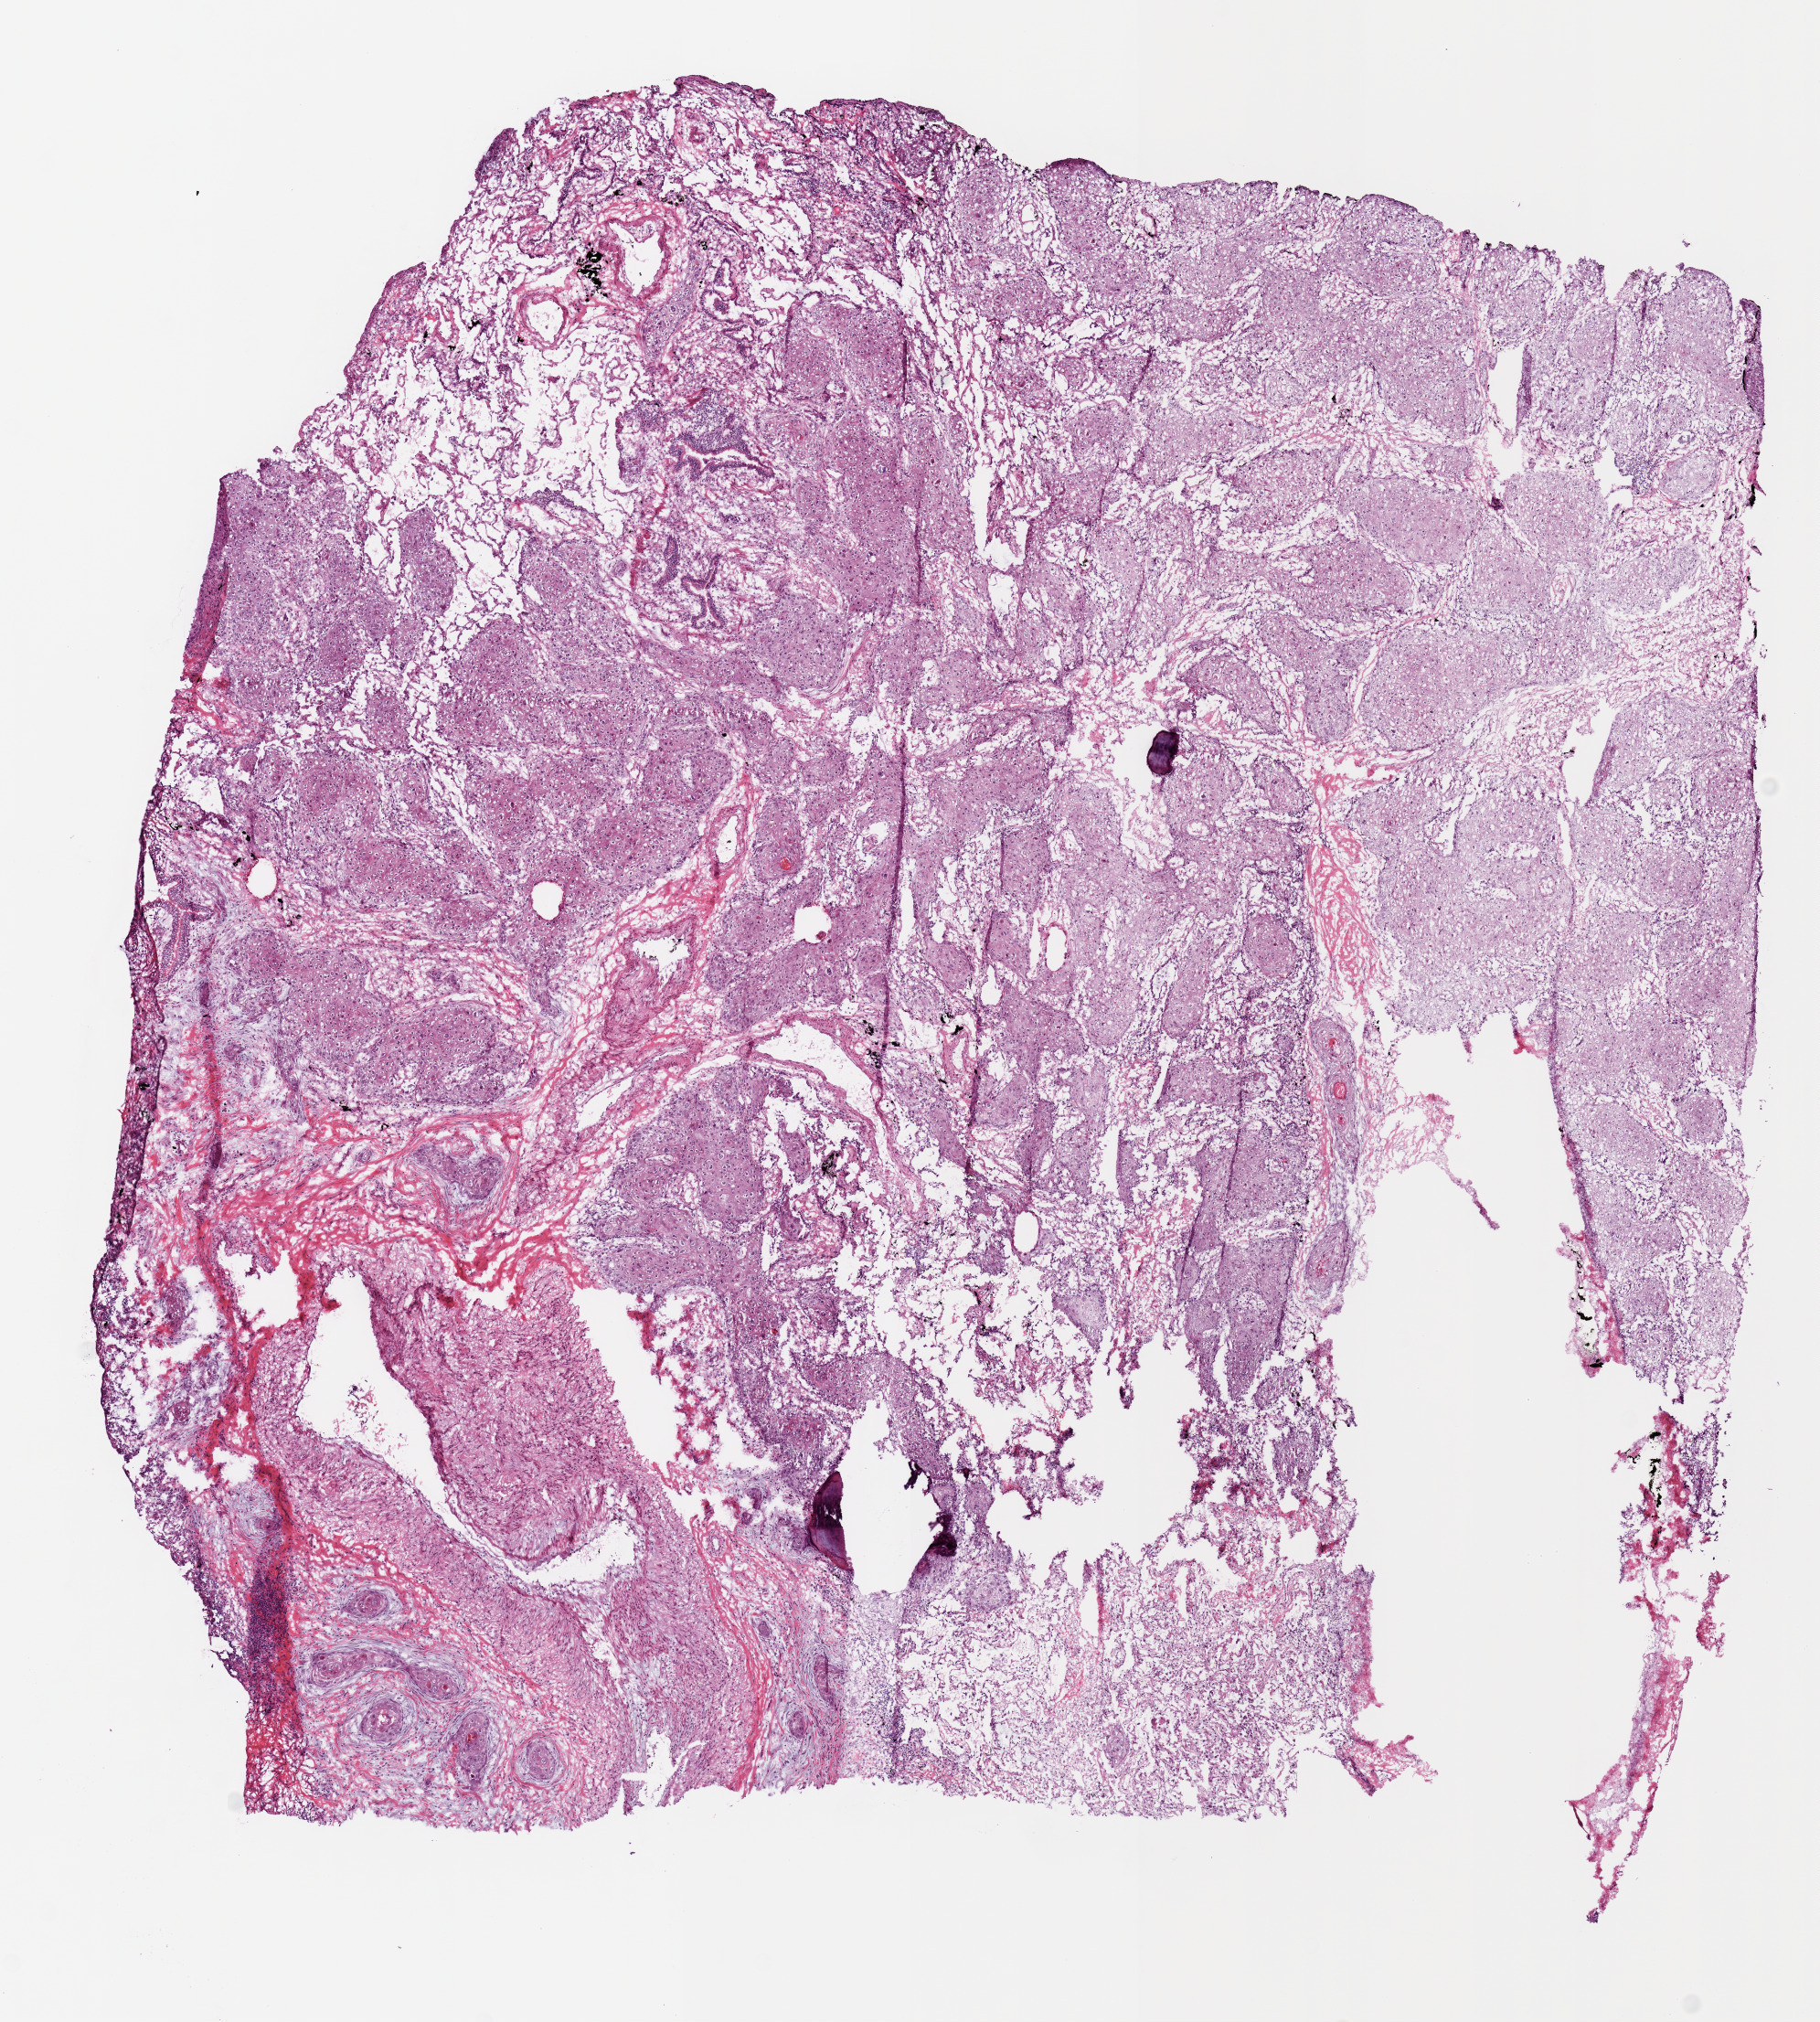
Whole-slide histology image, Hematoxylin and eosin (H&E) stained — a low-resolution overview of the entire scanned area, about 7.9 x 8.7 mm (slide scanned at 20x). Frozen section from the top of the tissue portion. Sample: primary tumour, lung. Male, age 84 years at initial diagnosis. Slide review estimates, as recorded: tumour nuclei 75%, necrosis 0%.
* diagnosis: Squamous cell carcinoma, NOS (lower lobe, lung)
* AJCC pathologic stage: IIB (7th edition)